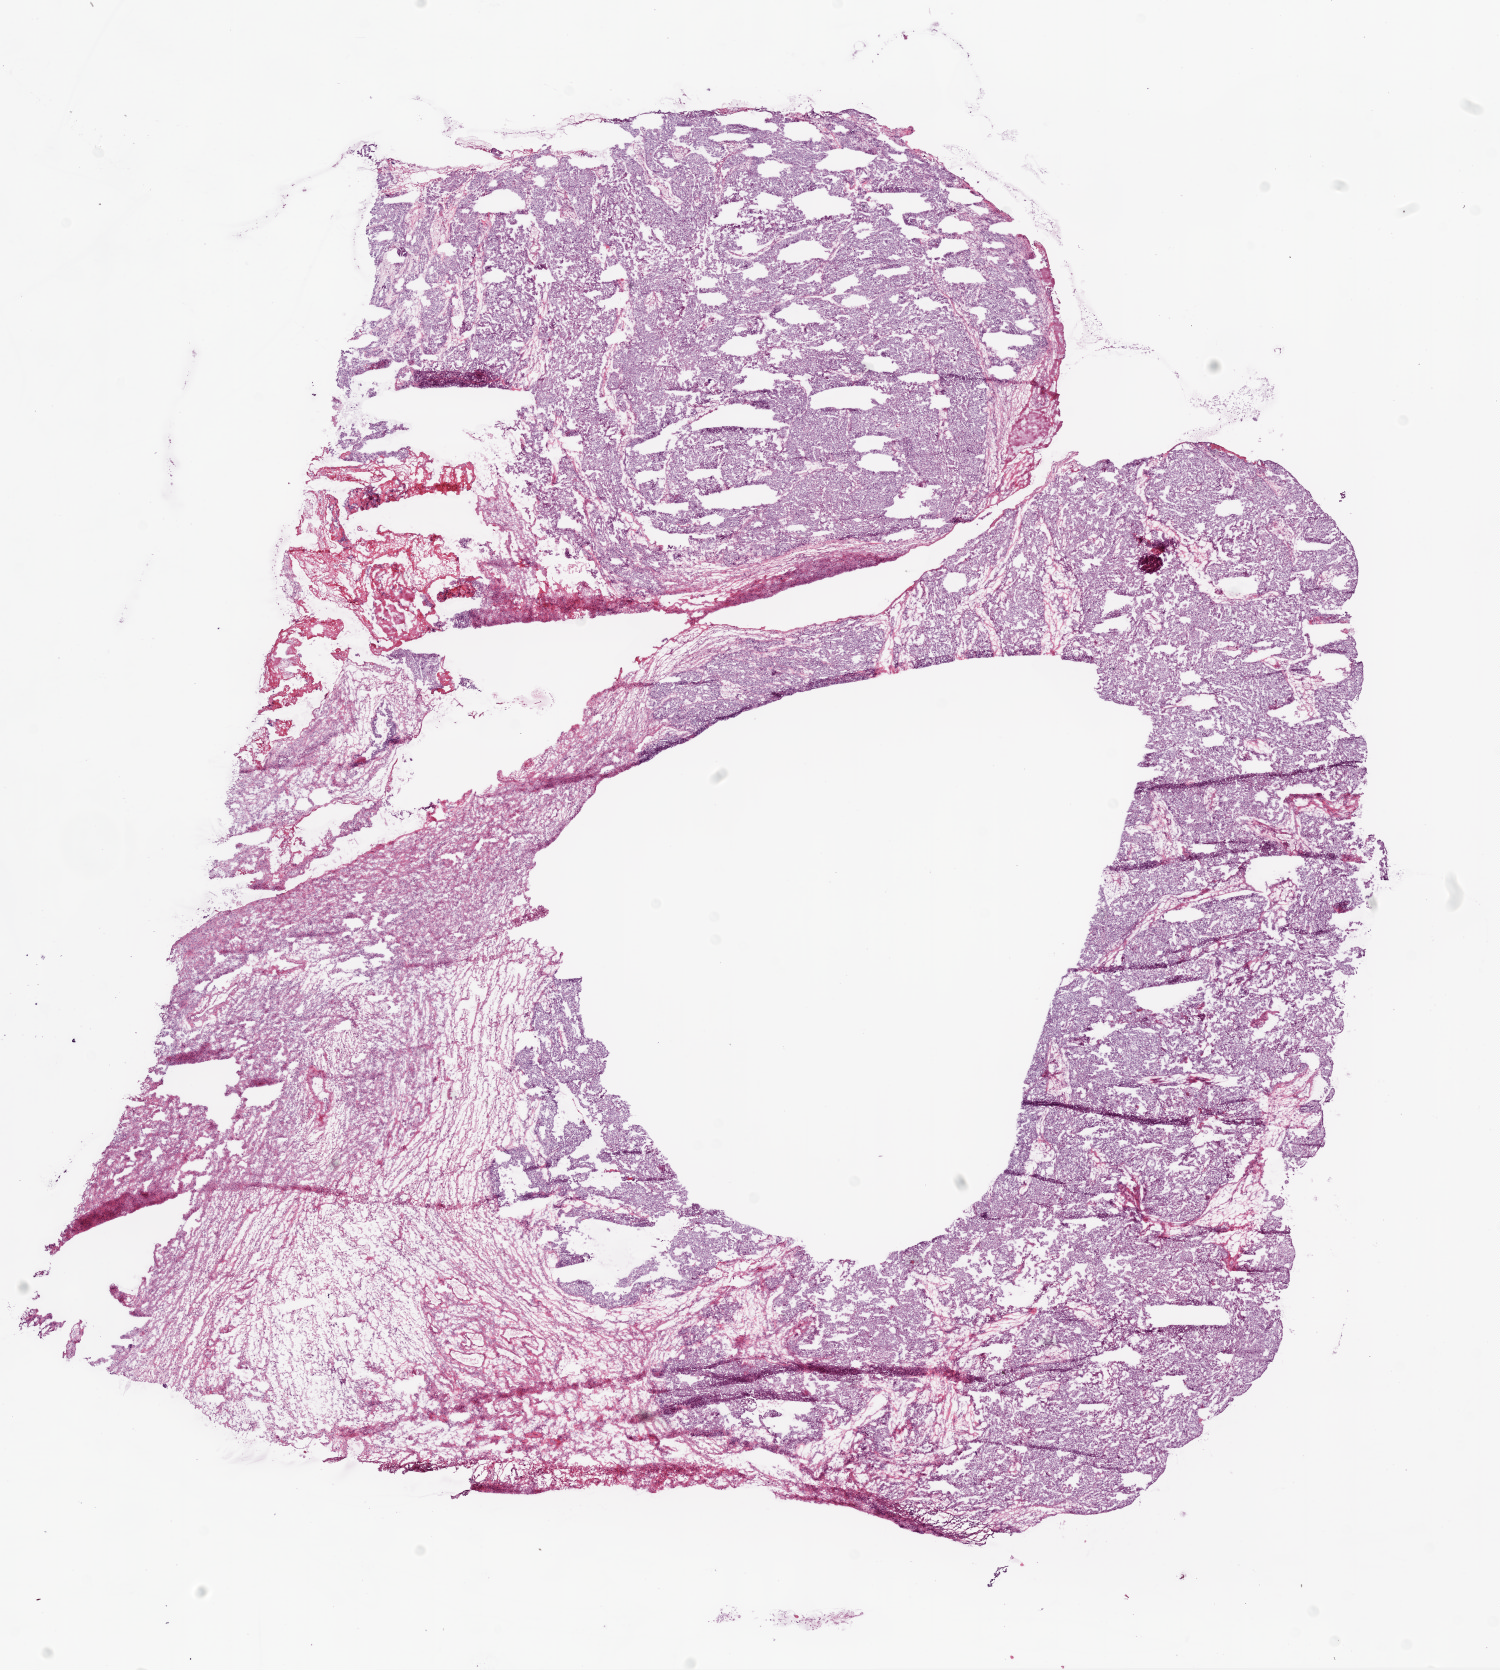
Digitized H&E tissue section (whole slide) — a low-resolution overview of the entire scanned area, about 12.0 x 13.4 mm. Frozen section from the bottom of the tissue portion. Ovary, primary tumour sample. Female, age 55 years at initial diagnosis. Histologic grade: G3 (poorly differentiated). Pathologist review of this section (percent, as recorded): tumour cells 80%, tumour nuclei 80%, normal cells 0%, stromal cells 20%, necrosis 0%.
- diagnosis: Serous cystadenocarcinoma, NOS
- laterality: bilateral
- FIGO stage: IIIC